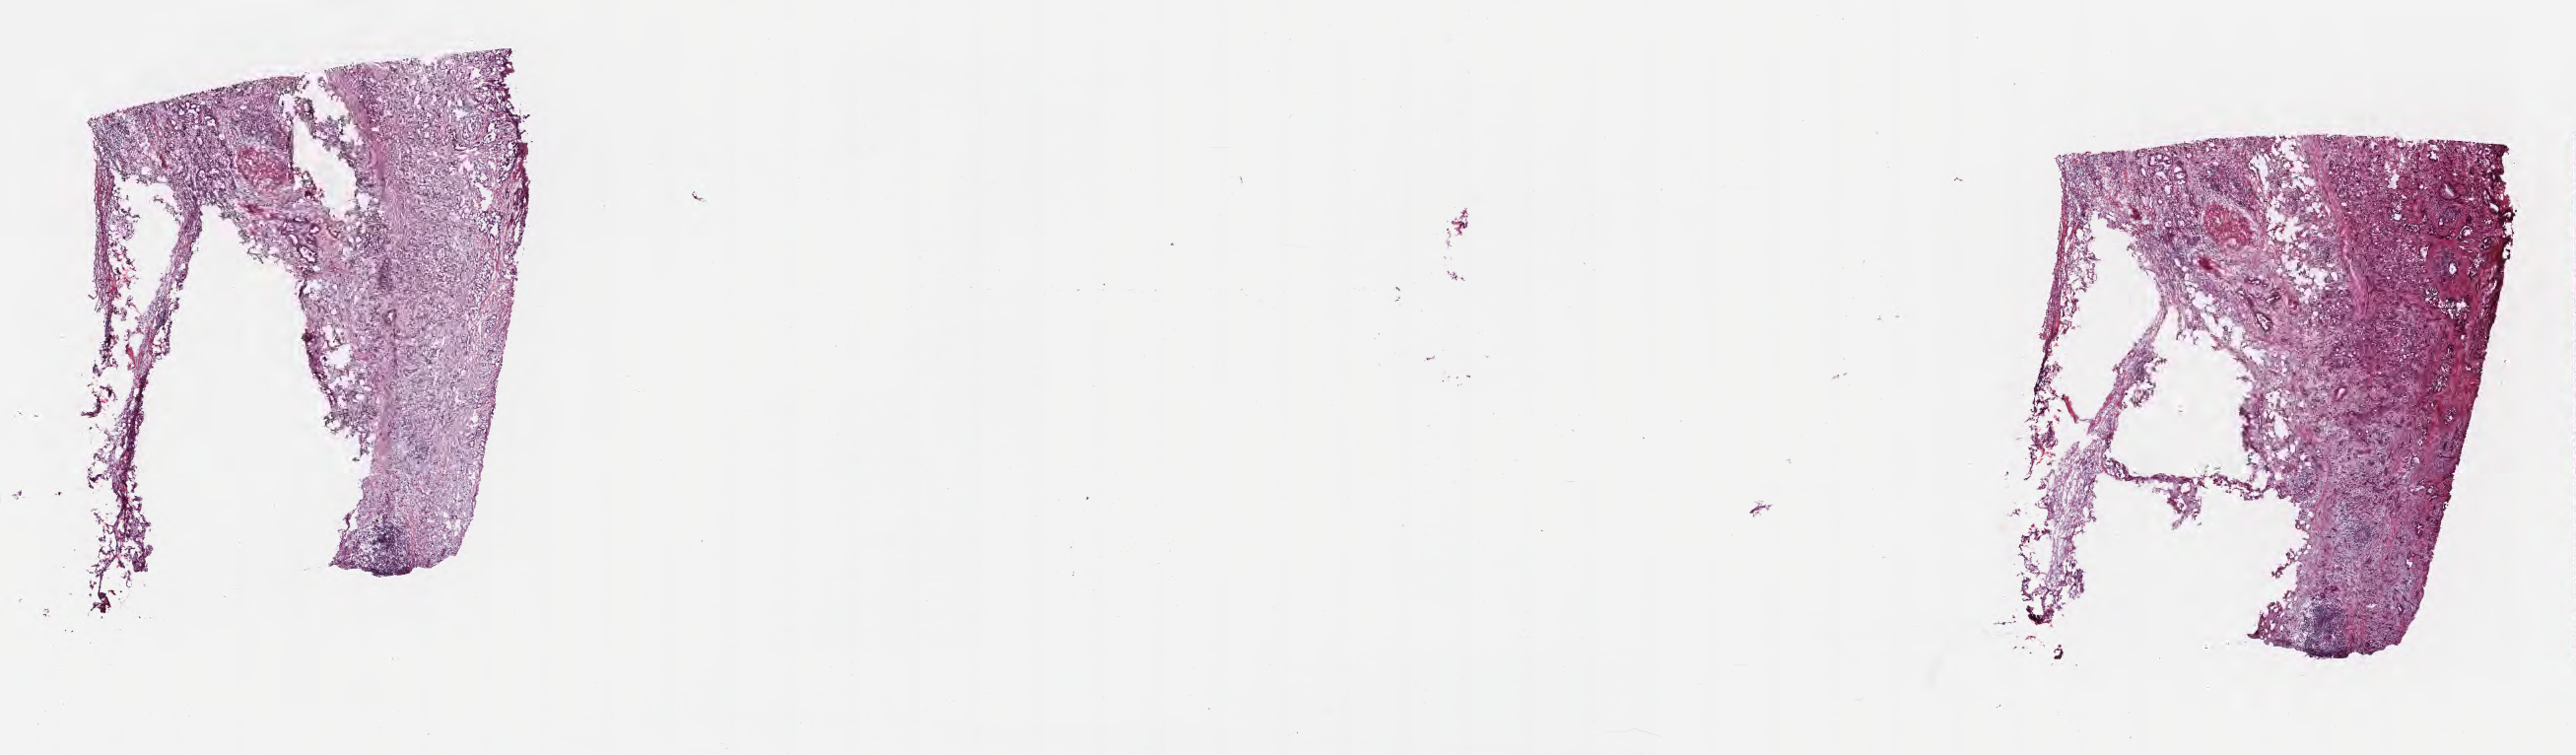
Whole-slide image, hematoxylin and eosin (H&E) stain — shown as a low-resolution overview of the whole scanned area (about 21.1 x 6.2 mm), cryosection, primary tumor, site: head of pancreas. Patient: male, age at initial diagnosis 62 years. Tumor grade: G3 (poorly differentiated). Slide review estimates, as recorded: tumor cells 15%, tumor nuclei 80%, stromal cells 85%, necrosis 0%, normal cells 0%. Infiltration values recorded for this section: lymphocyte infiltration 0%, monocyte infiltration 0%, neutrophil infiltration 0%.
AJCC pathologic stage: Stage III. Diagnosis: Infiltrating duct carcinoma, NOS.